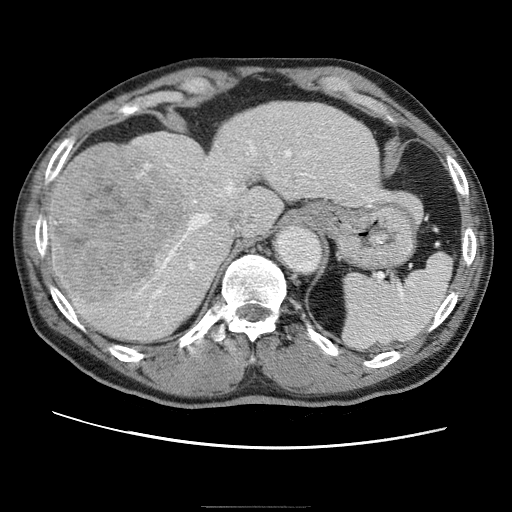
Contrast-enhanced abdominal CT (liver protocol), one axial slice; position 44 of 75 along the scan axis; reconstruction kernel STANDARD; 120 kVp; one of 2 acquisitions stored at this slice position; soft-tissue window (W 400 / L 40 HU); 2.5 mm slice thickness; 512 × 512 image matrix, field of view 360 × 360 mm. Case-level facts recorded for this patient, not image findings: diagnosis: hepatocellular carcinoma (patient treated with transarterial chemoembolisation; whether this scan precedes or follows treatment is not stated here); TNM stage (as recorded): Stage-II; Child-Pugh class: A; tumour differentiation: well differentiated; tumour nodularity: multinodular.
Structures marked on this image (semi-automatically segmented with operator editing):
- abdominal aorta: box from (x=276, y=227) to (x=320, y=272) px
- liver parenchyma outside the tumour (the mass and vessels are separate outlines, so this box may not span the whole liver): (x=49, y=102)–(x=384, y=342)
- mass: (x=49, y=148)–(x=184, y=298)
- liver vessels: (x=157, y=137)–(x=335, y=291)